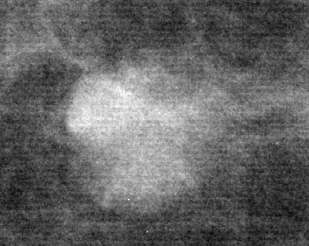
Cropped region of a digitized screen-film mammogram centred on a radiologist-marked abnormality; right breast; CC view; BI-RADS breast density category 2 (scale 1–4).
- Finding: mass, shape lobulated, margins circumscribed; BI-RADS assessment category 2; benign without callback (not worked up further).